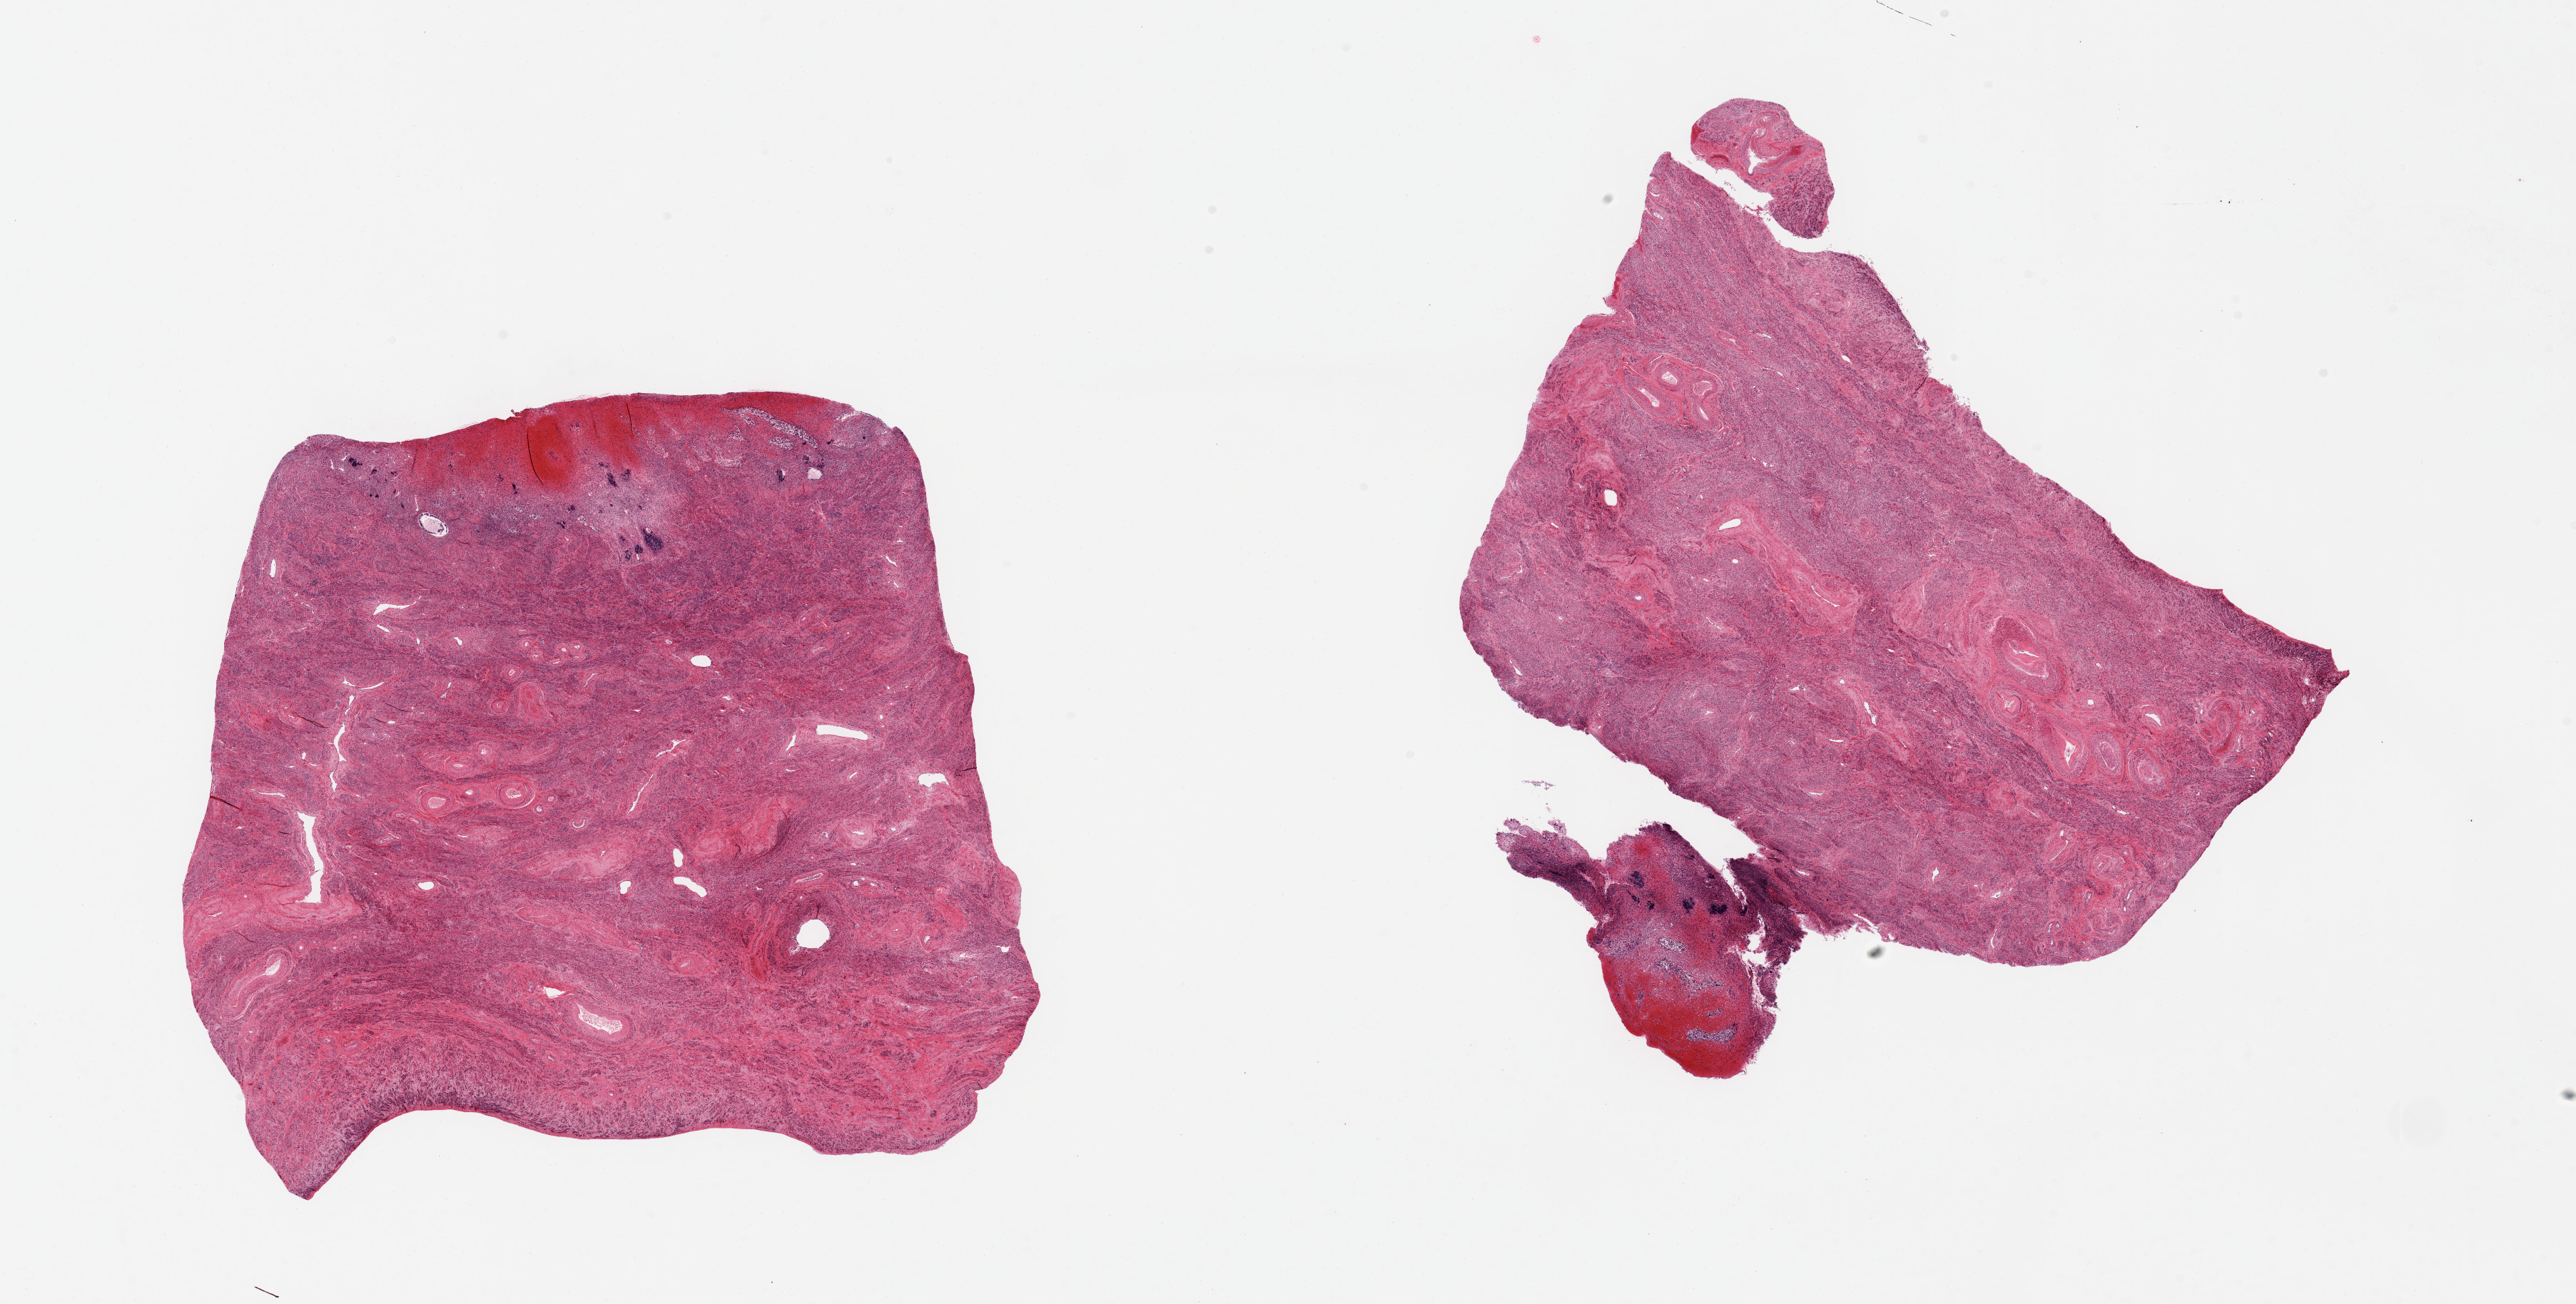
Digitized haematoxylin and eosin-stained section, brightfield — a low-resolution overview of the entire scanned area, about 28.5 x 14.5 mm. PAXgene-fixed paraffin-embedded (PFPE) section. Target tissue: uterus. Tissue donor sample. Female donor.
Reviewer comment on this tissue sample: 2 pieces; hemorrhagic & autolyzed endometrium; muscle intact.